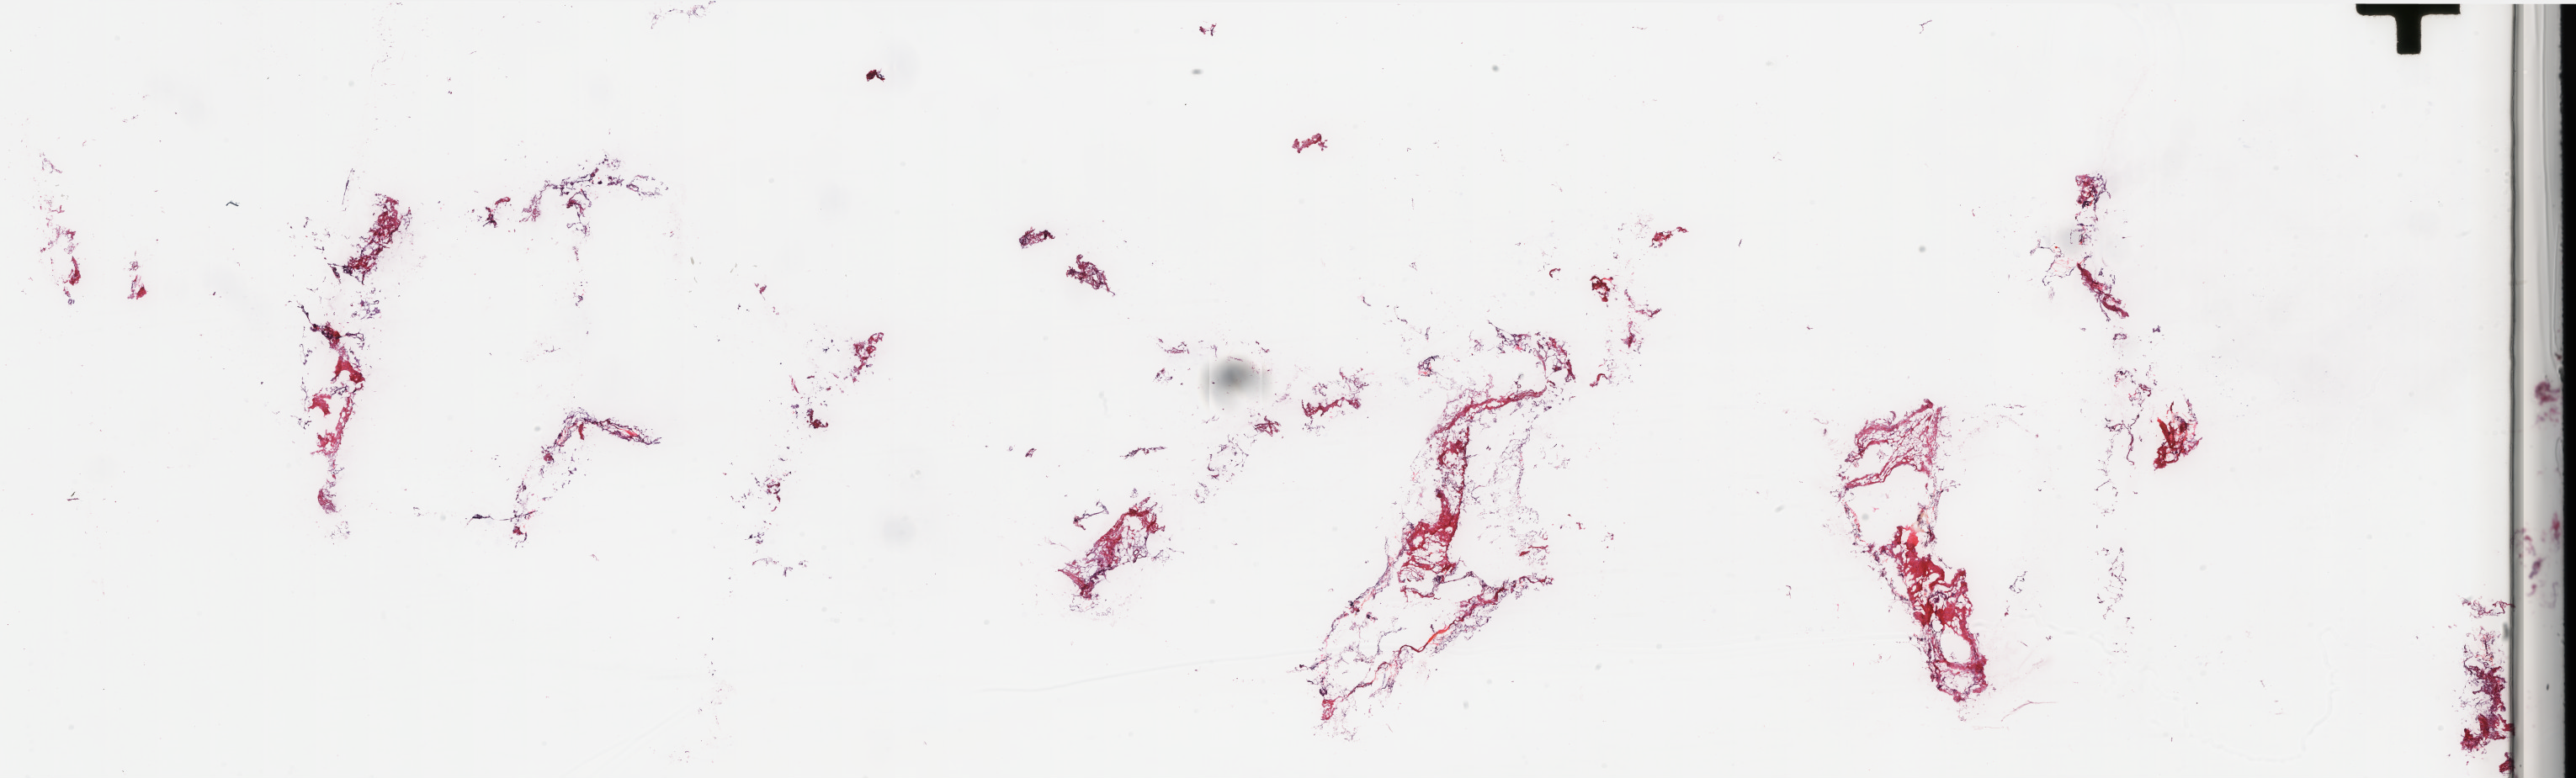
Whole-slide histology image, Hematoxylin and eosin (H&E) stained — a low-resolution overview of the entire scanned area, about 48.9 x 14.8 mm; frozen section; breast, solid tissue normal (non-tumour tissue) sample. Female, age 37 years at initial diagnosis. Pathologist review of this section (percent, as recorded): tumour cells 0%, tumour nuclei 0%, normal cells 0%, stromal cells 100%, necrosis 0%. Infiltration values recorded for this section: lymphocyte infiltration 1%, monocyte infiltration 0%, neutrophil infiltration 0%.
This section: solid tissue normal sample (biorepository sample class). Patient diagnosis: Infiltrating duct carcinoma, NOS.